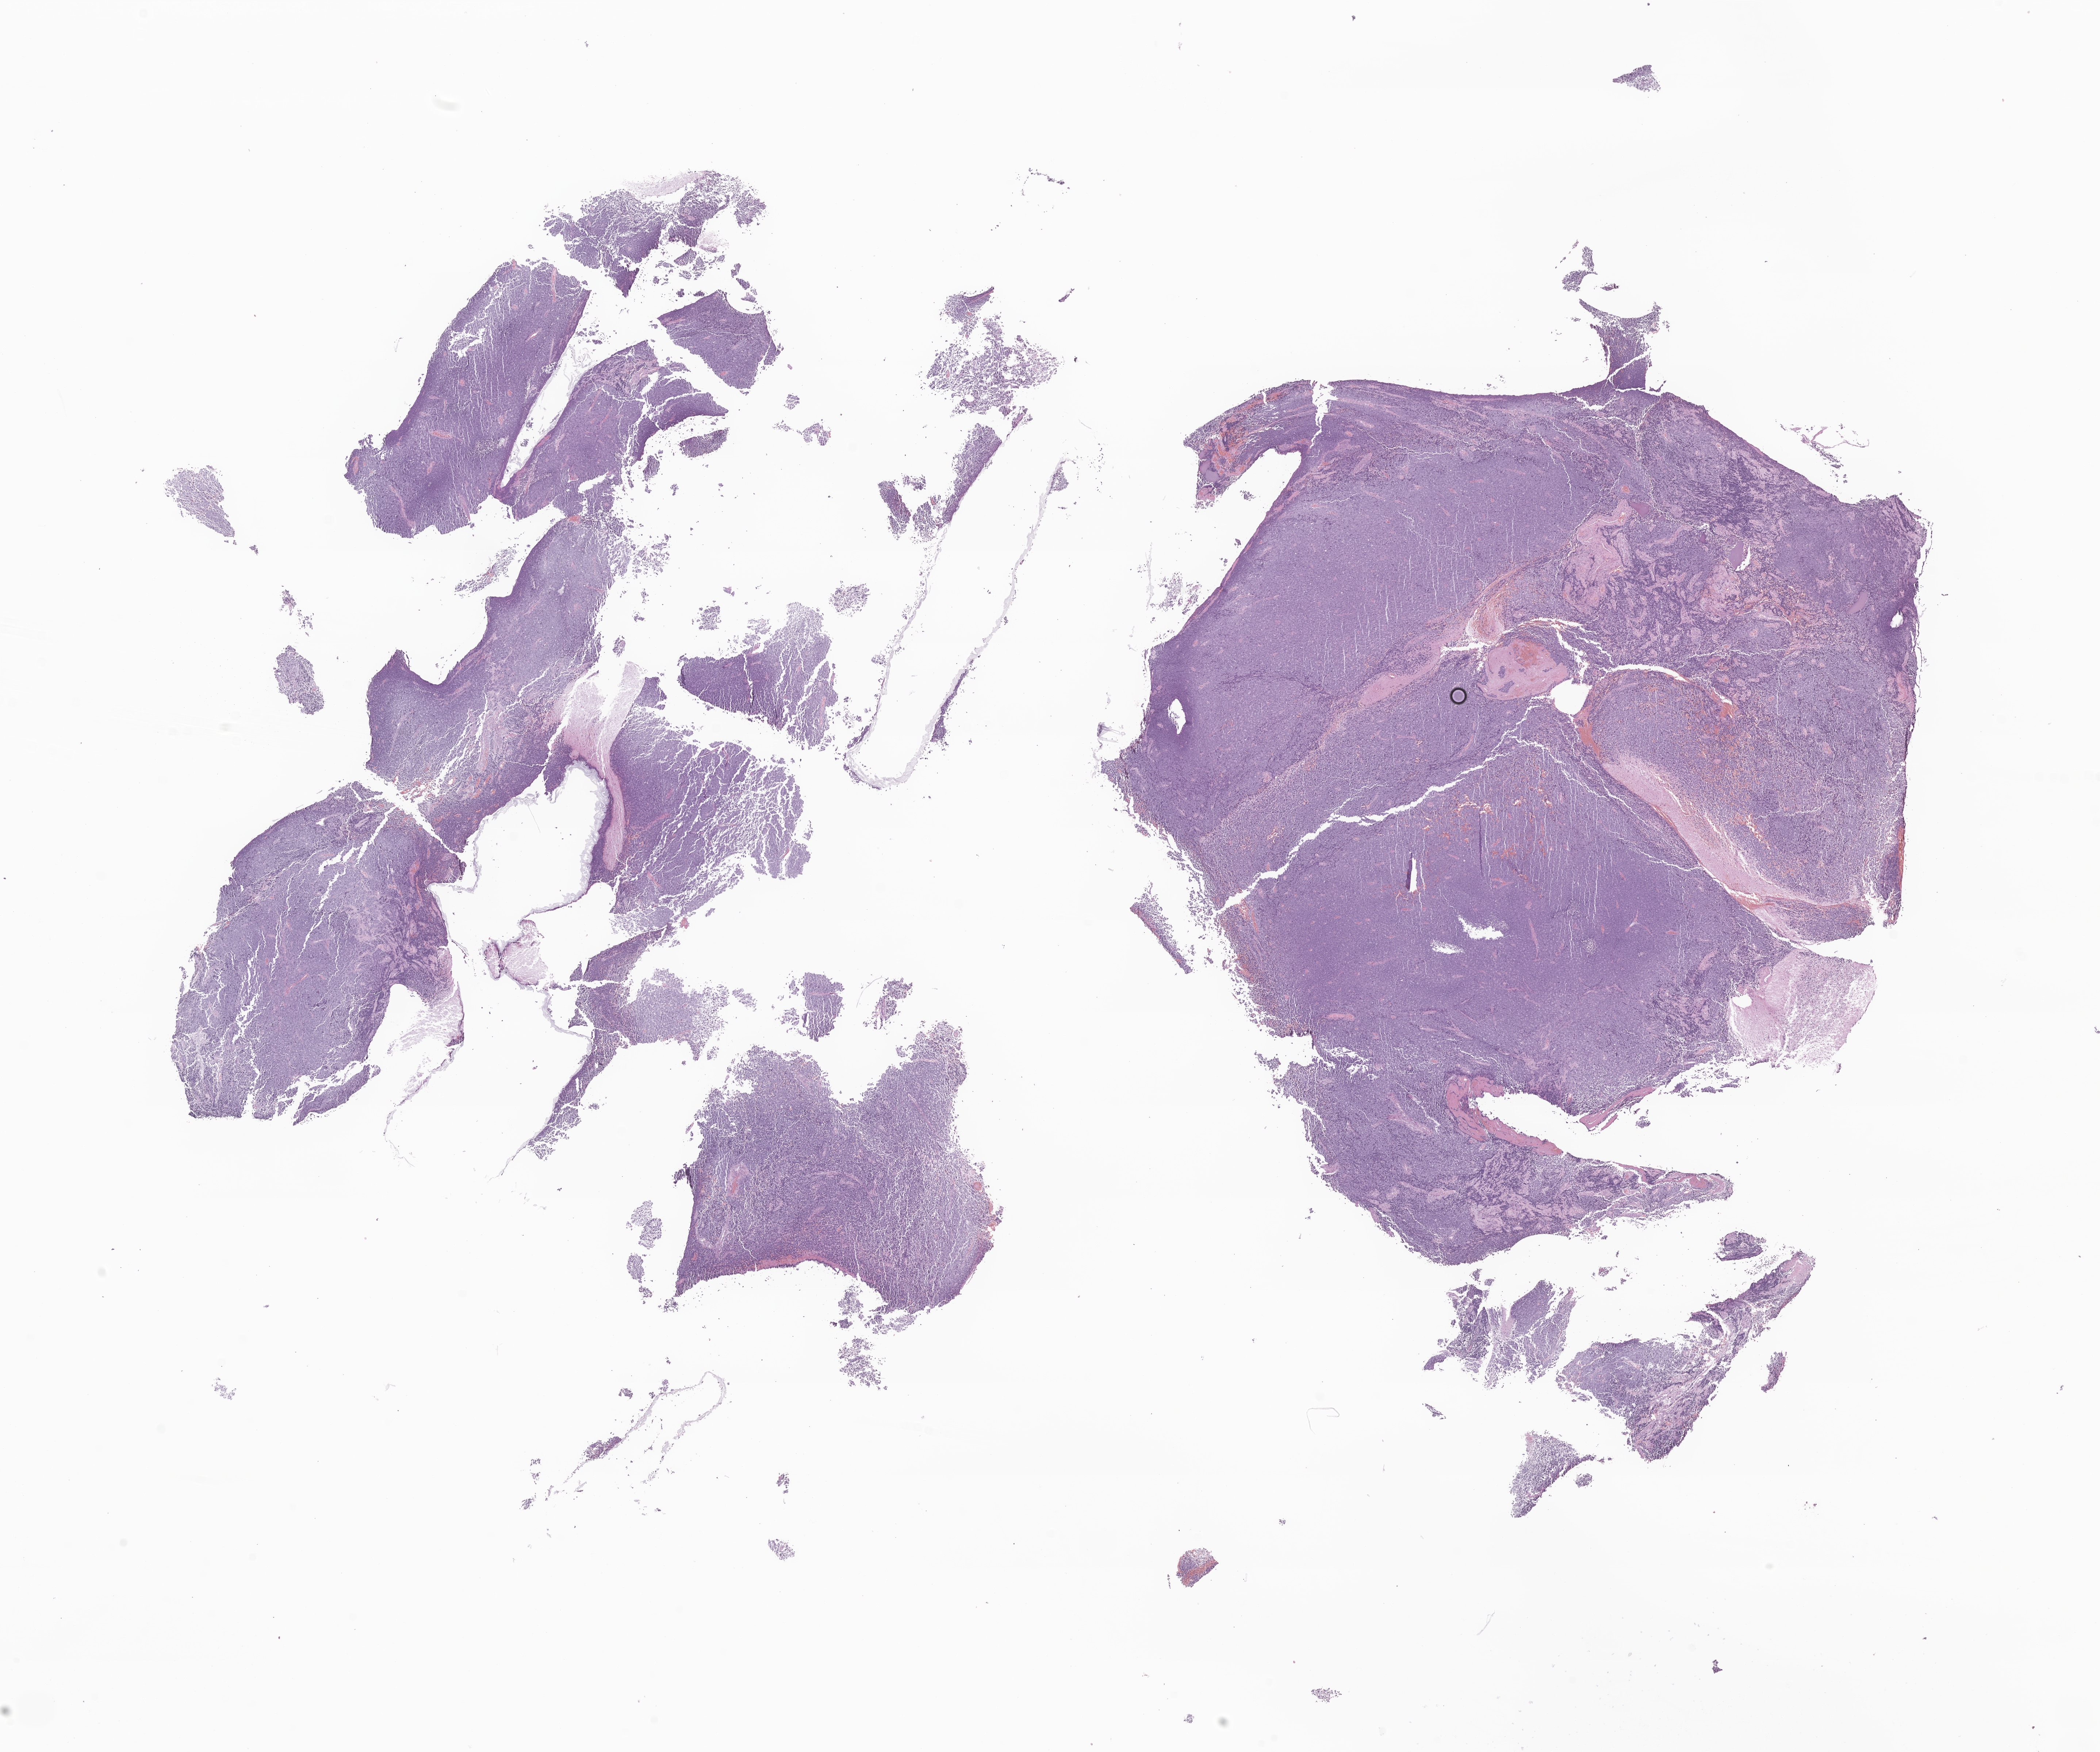
Digitized hematoxylin and eosin (H&E)-stained section of tumor tissue from the brain — a low-resolution overview of the entire scanned area, about 24.2 x 20.2 mm, formalin-fixed, paraffin-embedded (FFPE) tissue. Male patient, age 184 months (15 years 4 months).
Diagnosis (ICD-O-3 morphology term): Medulloblastoma, NOS.